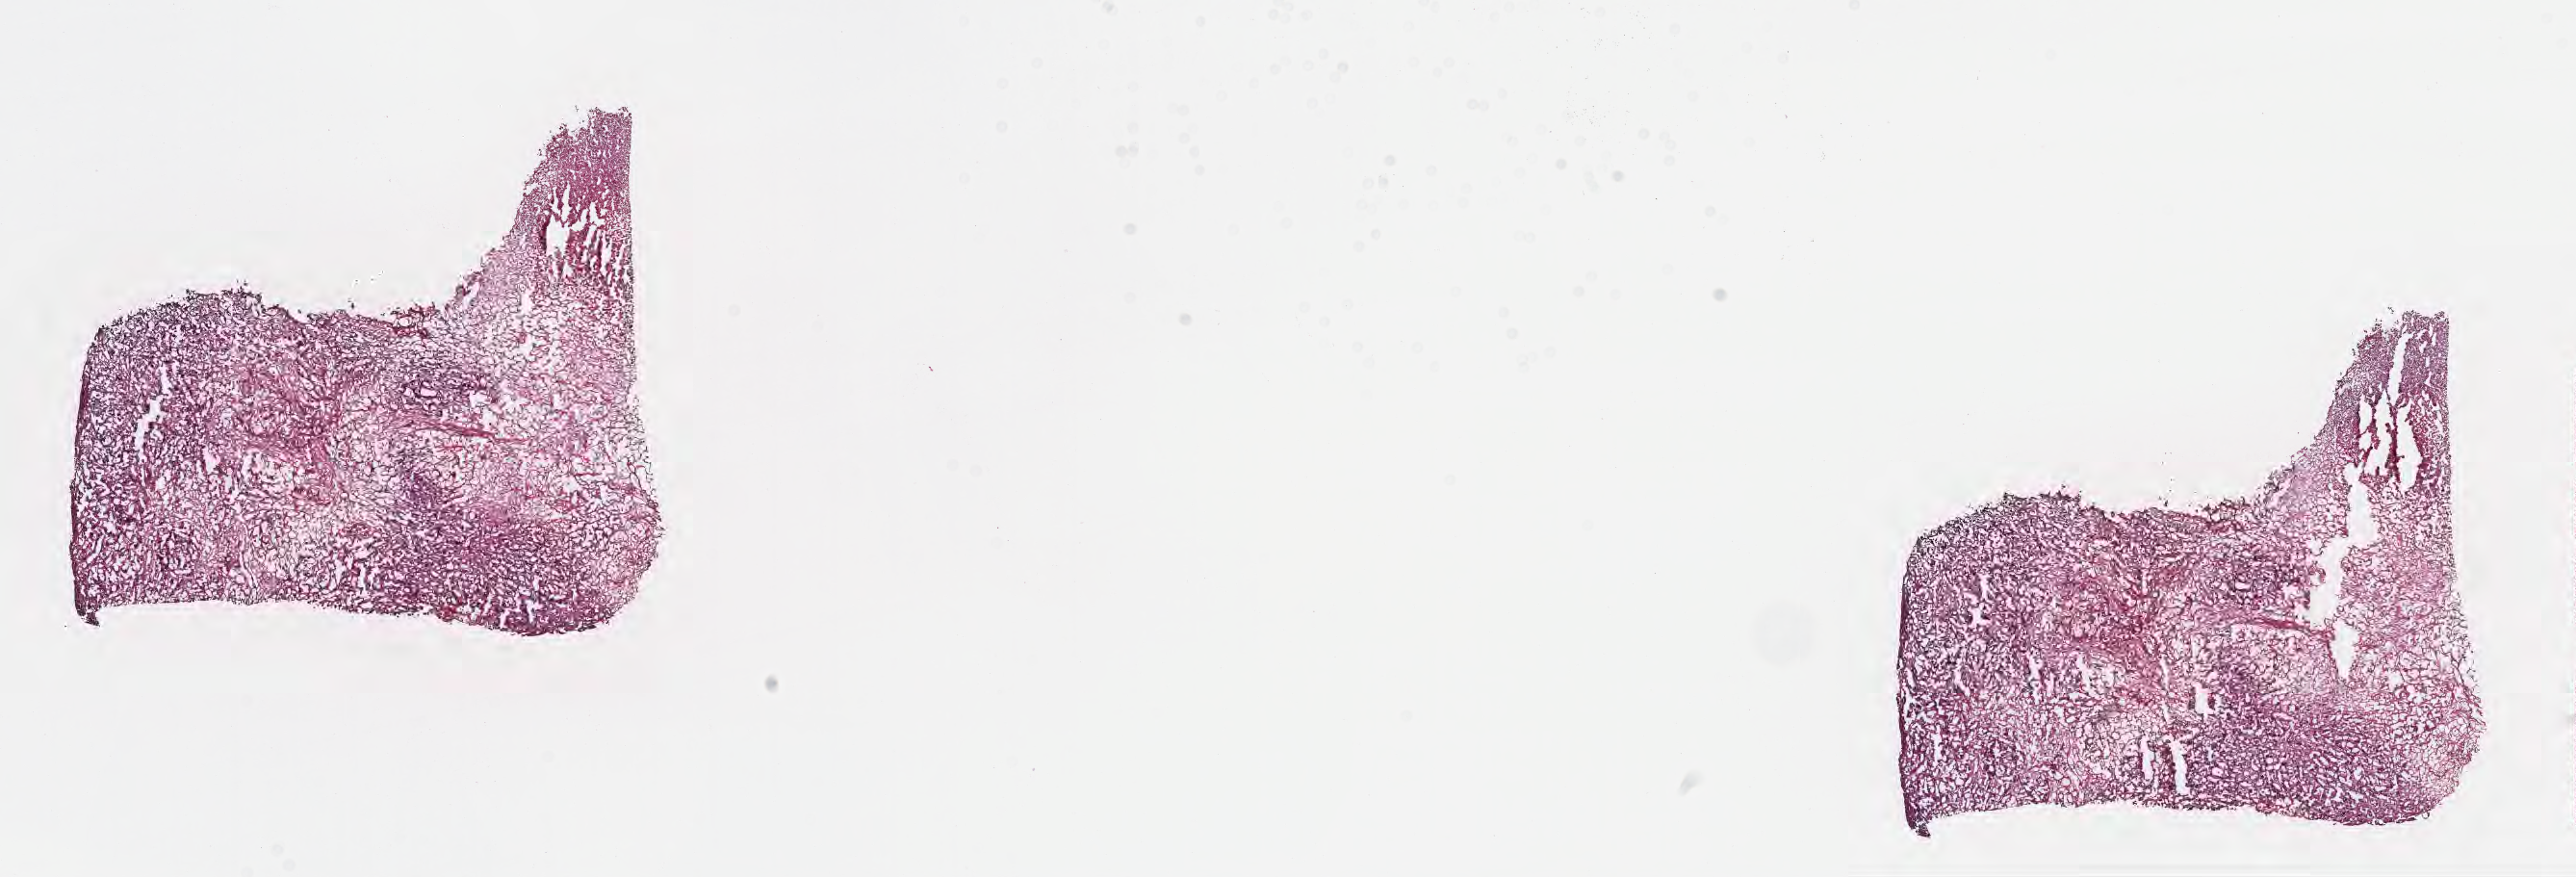
Digitized hematoxylin and eosin (H&E)-stained section — shown as a low-resolution overview of the whole scanned area (about 21.6 x 7.4 mm); frozen section (tissue freezing medium); specimen: primary tumor; site: extrahepatic bile duct. Female, age 64 years at initial diagnosis. Composition of this section per pathologist review: tumor cells 30%, tumor nuclei 40%, stromal cells 70%, necrosis 0%, normal cells 0%. Inflammatory infiltration, as recorded: lymphocyte infiltration 0%, monocyte infiltration 0%, neutrophil infiltration 0%.
• AJCC pathologic stage: Stage IIIB
• histologic diagnosis: Cholangiocarcinoma